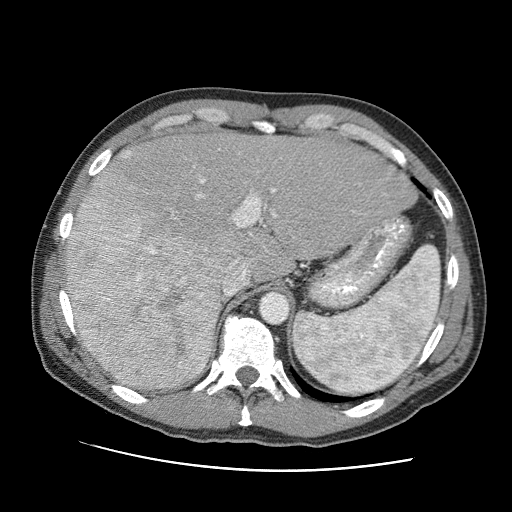
Contrast-enhanced abdominal CT (liver protocol), one axial slice; reconstruction kernel STANDARD; one of 2 acquisitions stored at this slice position; soft-tissue window (W 400 / L 40 HU); 2.5 mm slice thickness; 512 × 512 image matrix. From the clinical record (not read from this slice): diagnosis: hepatocellular carcinoma (patient treated with transarterial chemoembolisation; whether this scan precedes or follows treatment is not stated here); TNM stage (as recorded): Stage-IVA; Child-Pugh class: A; tumour differentiation: moderately differentiated; tumour nodularity: multinodular.
Annotated regions visible in this slice (semi-automatic segmentation, software-assisted and operator-edited):
- liver parenchyma outside the tumour (the mass and vessels are separate outlines, so this box may not span the whole liver): bounding box [x1, y1, x2, y2] px = [66, 130, 416, 388]
- mass: [65, 148, 230, 390]
- liver vessels: [180, 178, 277, 290]